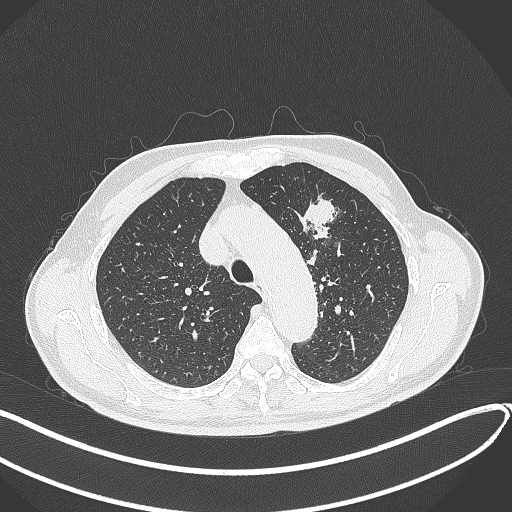
Chest CT, one axial slice; slice 313 of 459 in the series (ordered by position); 120 kVp; lung window (W 1500 / L -600 HU); 1 mm slice thickness; 512 × 512 image matrix, field of view 400 × 400 mm. Patient: male, 74 years. From the clinical record (not read from this slice): clinical TNM (as recorded): T2b N0 M1c.
Structures marked on this image (bounding box drawn by a radiologist):
- lung tumour (recorded histology: adenocarcinoma): bounding box <297,193,341,250> (left, top, right, bottom; pixels)